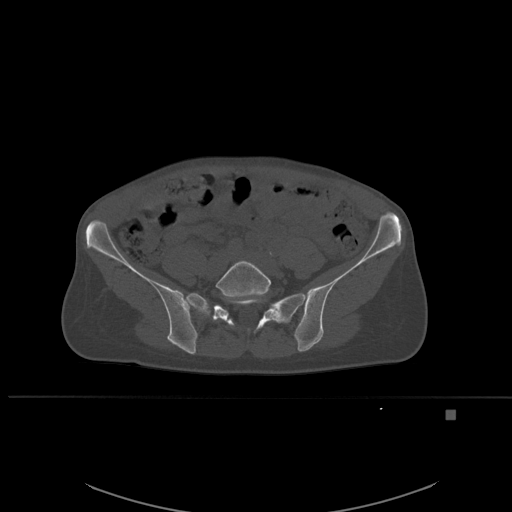
CT including the spine, one axial slice. Position 165 of 537 along the scan axis. Bone window (W 1800 / L 400 HU). 1.5 mm slice thickness. 512 × 512 image matrix, field of view 440 × 440 mm. Patient: female, 45 years. From the clinical record (not read from this slice): primary cancer: lung.
Outlined on this slice (semi-automatically segmented with operator editing):
- L5 vertebra: box from (x=216, y=260) to (x=272, y=331) px